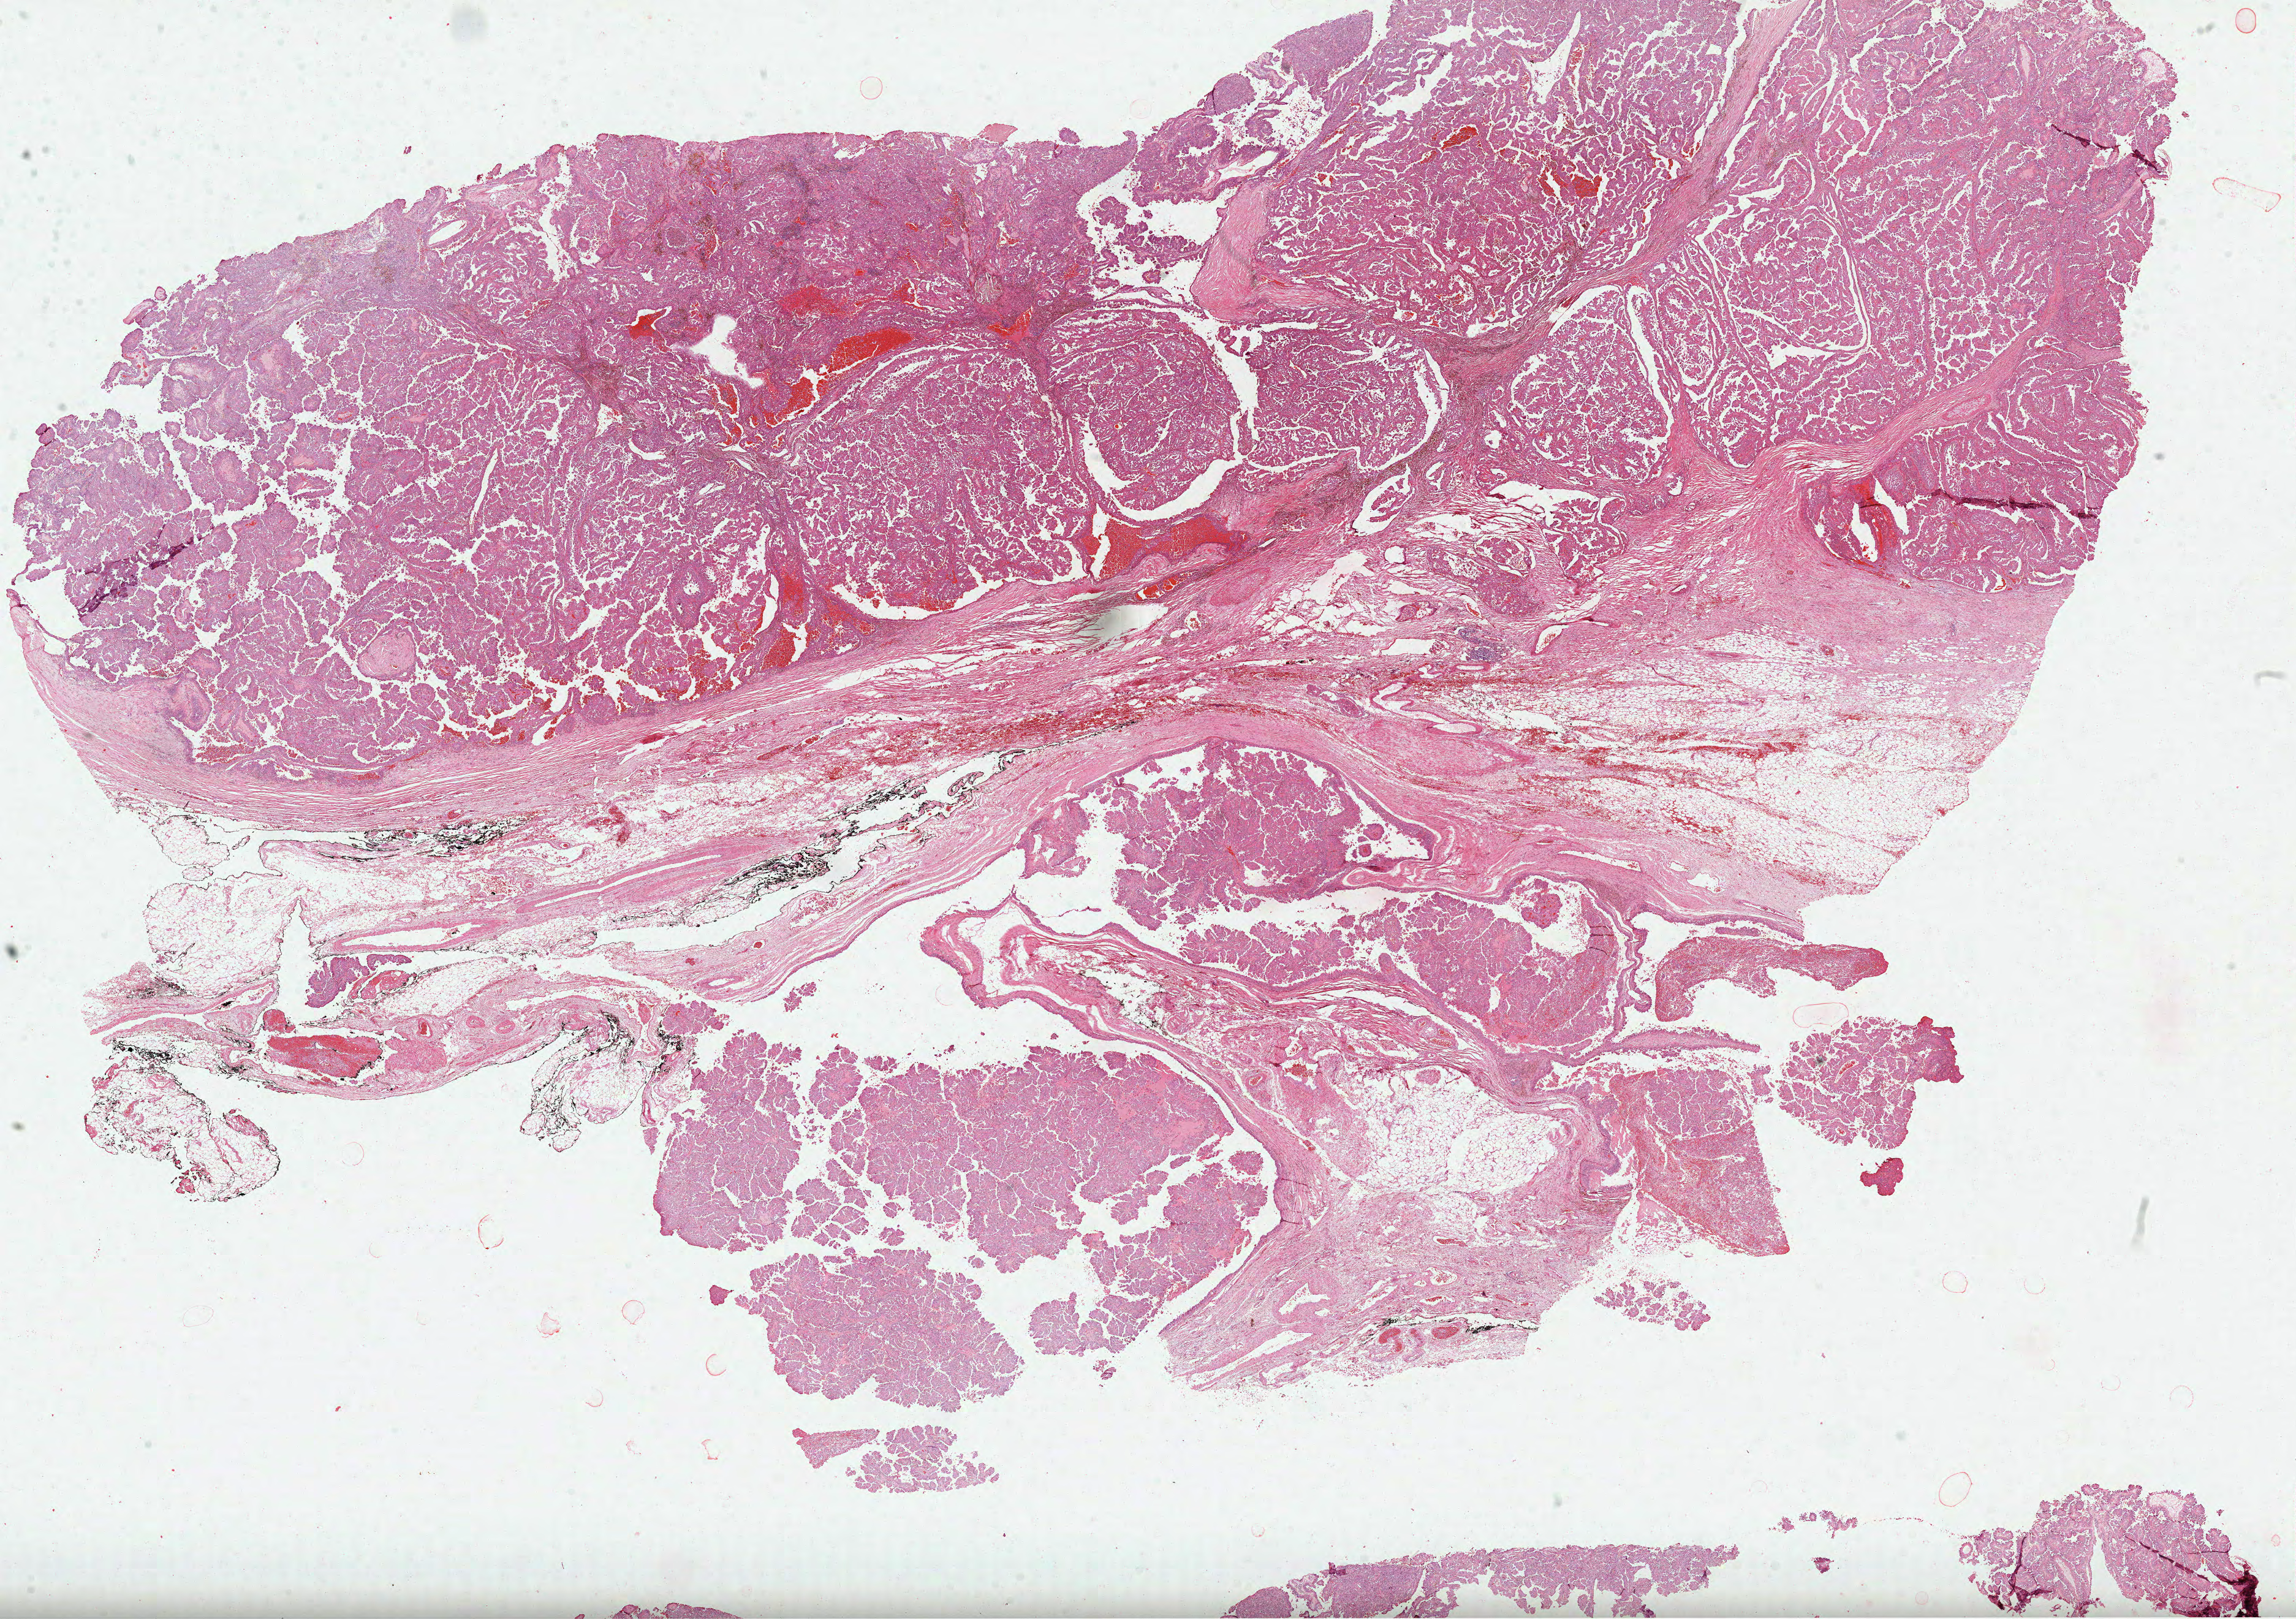
Digitized H&E-stained tissue section (whole slide), shown as a low-resolution overview of the whole scanned area (about 30.2 x 21.3 mm, acquisition: 40x scan), formalin-fixed paraffin-embedded (FFPE) diagnostic section, primary tumour sample from the kidney. Female, age 60 years at initial diagnosis.
AJCC pathologic stage: IV. Pathologic diagnosis: Papillary adenocarcinoma, NOS.